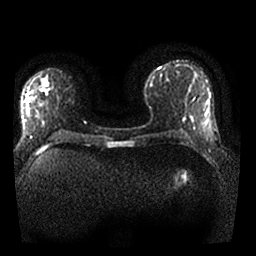
Breast MRI, one axial slice; slice 10 of 25 in the series (ordered by position); diffusion-weighted series; image 2 of 4 stored at this slice position (different b-values; order by instance number); 1.5 T; 256 × 256 image matrix, field of view 330 × 330 mm. Female patient.
Annotated regions visible in this slice (outlined manually by an expert reader):
- tumour on diffusion-weighted imaging: bounding box (x1, y1, x2, y2) in pixels: (44, 84, 48, 91)